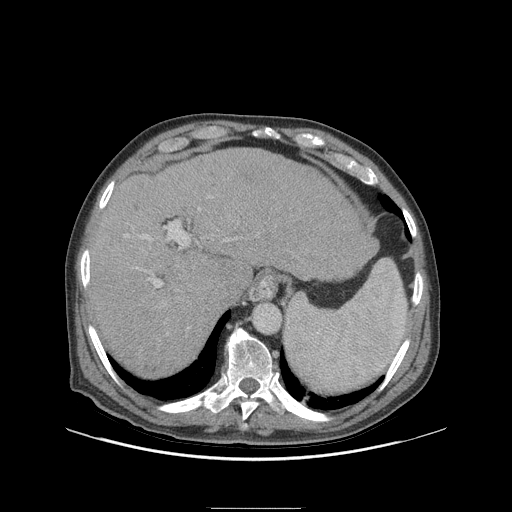
Contrast-enhanced abdominal CT (liver protocol), one axial slice; position 75 of 105 along the scan axis; reconstruction kernel STANDARD; soft-tissue window (W 400 / L 40 HU); 2.5 mm slice thickness; 512 × 512 image matrix, field of view 440 × 440 mm. From the clinical record (not read from this slice): diagnosis: hepatocellular carcinoma (patient treated with transarterial chemoembolisation; whether this scan precedes or follows treatment is not stated here); TNM stage (as recorded): Stage-I; Child-Pugh class: A; tumour nodularity: uninodular; tumour size: 5.1 cm.
Annotated regions visible in this slice (semi-automatic segmentation, software-assisted and operator-edited):
- abdominal aorta: bounding box [x1, y1, x2, y2] px = [253, 303, 281, 333]
- liver parenchyma outside the tumour (the mass and vessels are separate outlines, so this box may not span the whole liver): [88, 148, 376, 376]
- liver vessels: [125, 208, 228, 288]